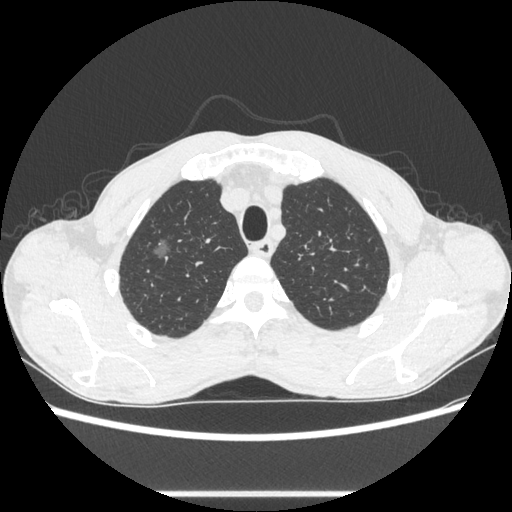
Chest CT, one axial slice; slice 496 of 600 in the series (ordered by position); 100 kVp; lung window (W 1500 / L -600 HU); 0.62 mm slice thickness; 512 × 512 image matrix, field of view 357 × 357 mm. Patient: male, 54 years. From the clinical record (not read from this slice): clinical TNM (as recorded): T1a N0 M0.
Outlined on this slice (bounding box drawn by a radiologist):
- lung tumour (recorded histology: adenocarcinoma): box from (x=145, y=223) to (x=172, y=271) px